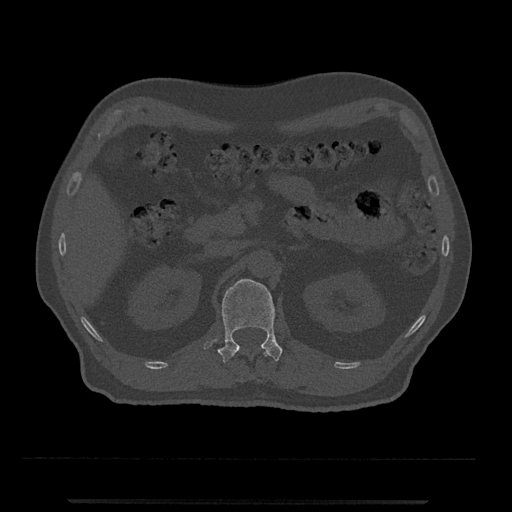
CT including the spine, one axial slice. Slice 351 of 797 in the series (ordered by position). Reconstruction kernel Br40s/3. Bone window (W 1800 / L 400 HU). 0.5 mm slice thickness. 512 × 512 image matrix, field of view 419 × 419 mm. Patient: male, 63 years. Case-level facts recorded for this patient, not image findings: primary cancer: prostate.
Annotated regions visible in this slice (semi-automatic segmentation, software-assisted and operator-edited):
- L1 vertebra: bounding box (x1, y1, x2, y2) in pixels: (204, 279, 283, 364)
- T12 vertebra: (264, 349, 269, 356)